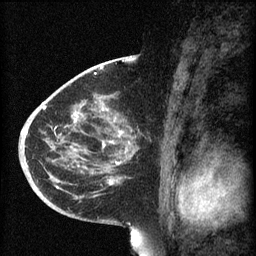
Breast MRI (dynamic contrast-enhanced), one sagittal slice. Position 37 of 60 along the scan axis. 3 images stored at this slice position (order not interpretable as contrast timing). 1.5 T. TE 4.2 ms, TR 8.1 ms. 2 mm slice thickness. 256 × 256 image matrix, field of view 200 × 200 mm. Female patient, age 44 years.
Annotated regions visible in this slice (semi-automatically segmented with operator editing):
- analysis volume of interest (the breast-tissue region the enhancement analysis was run in; not a lesion): box from (x=59, y=110) to (x=142, y=169) px
- tumour enhancement mask (voxels above the 70 % enhancement threshold inside the analysis volume of interest): (x=74, y=110)–(x=123, y=165)